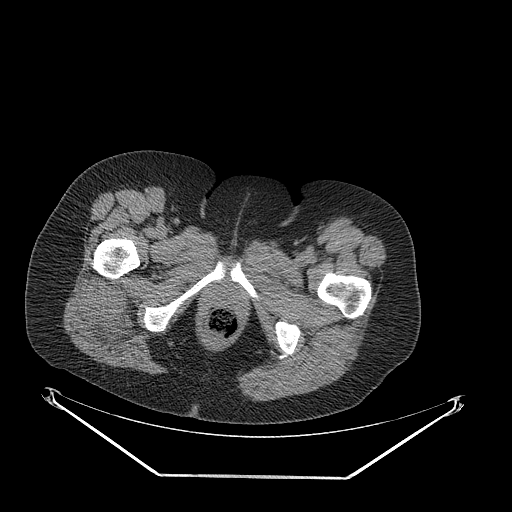
CT of an extremity soft-tissue mass (from a PET/CT study), one axial slice. Position 58 of 257 along the scan axis. Soft-tissue window (W 400 / L 40 HU). 3.75 mm slice thickness. 512 × 512 image matrix, field of view 500 × 500 mm. Female patient. Case-level facts recorded for this patient, not image findings: histological type: synovial sarcoma; grade: intermediate; site of the primary tumour: right buttock.
Annotated regions visible in this slice (expert contour drawn on MRI and transferred to this co-registered scan by the dataset authors):
- gross tumour volume including surrounding oedema: bounding box [x1, y1, x2, y2] px = [82, 276, 145, 348]
- gross tumour volume (mass): [82, 276, 136, 330]